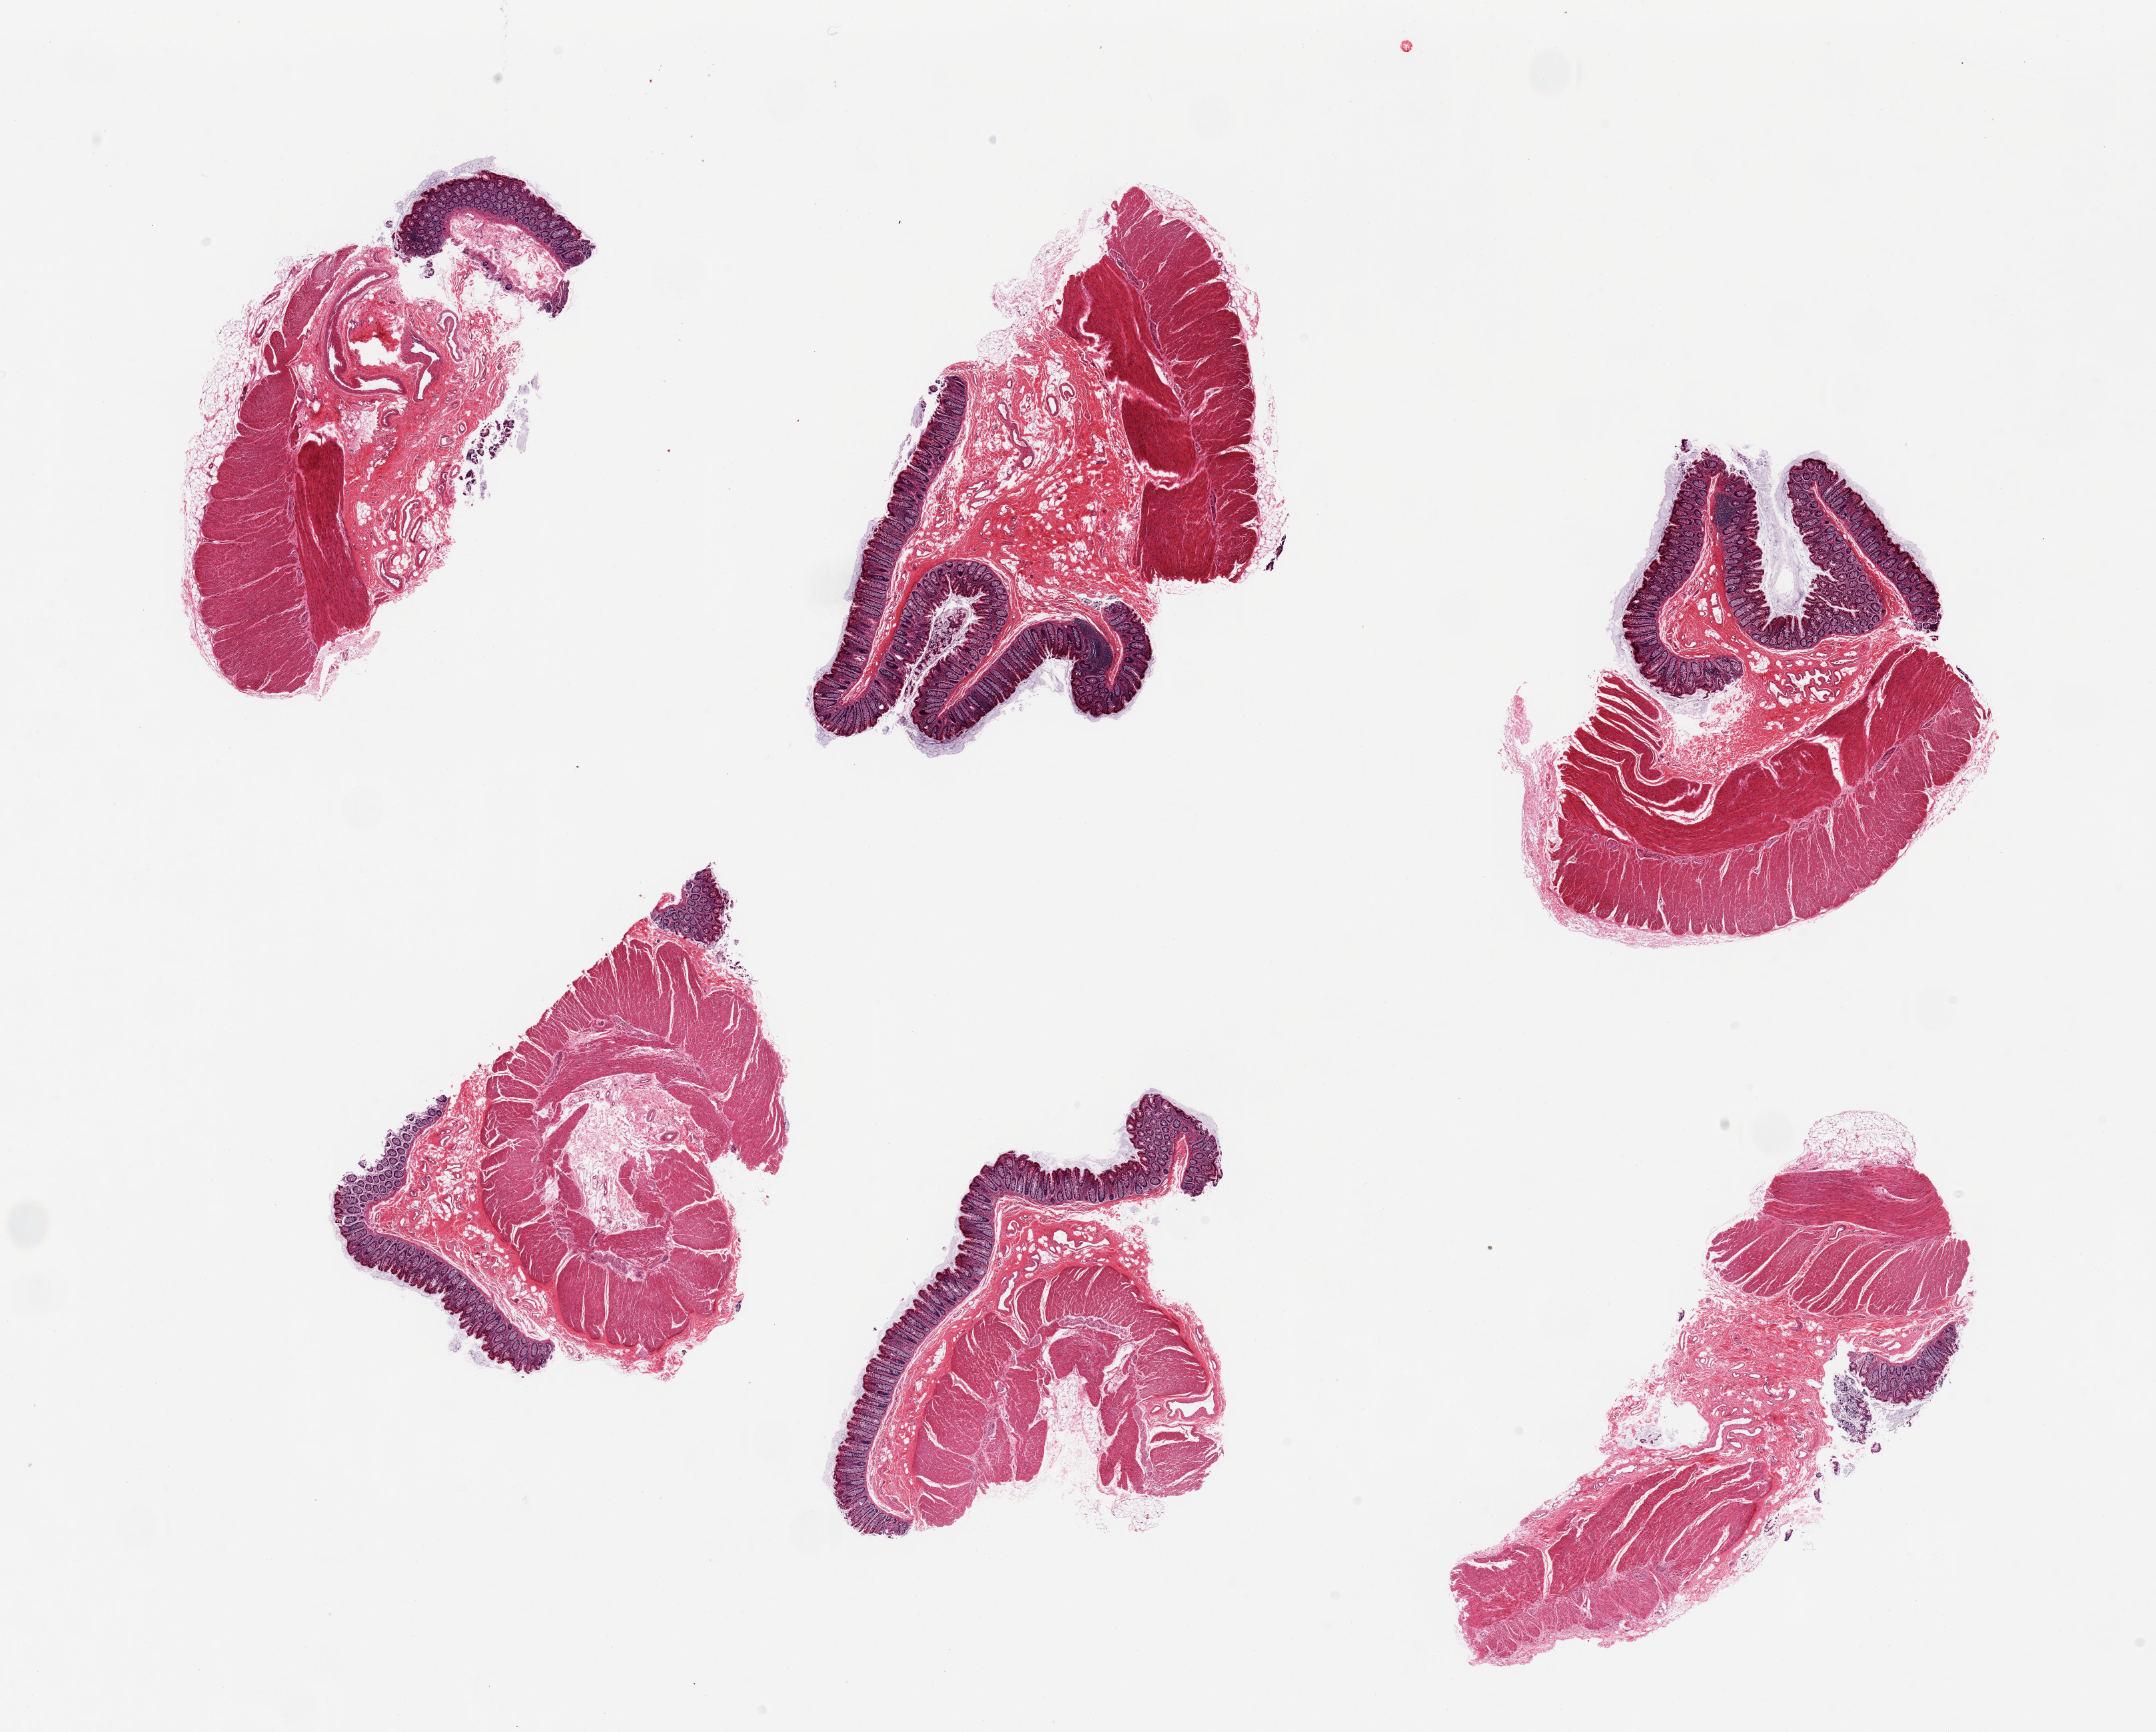
Digitized haematoxylin and eosin-stained section, brightfield, a low-resolution overview of the entire scanned area, about 25.6 x 20.6 mm, PAXgene-fixed, paraffin-embedded tissue, sampled site (target tissue): transverse colon, tissue donor sample. Donor: male.
• reviewer comment on this tissue sample: 6 pieces, all include mucosa and muscularis